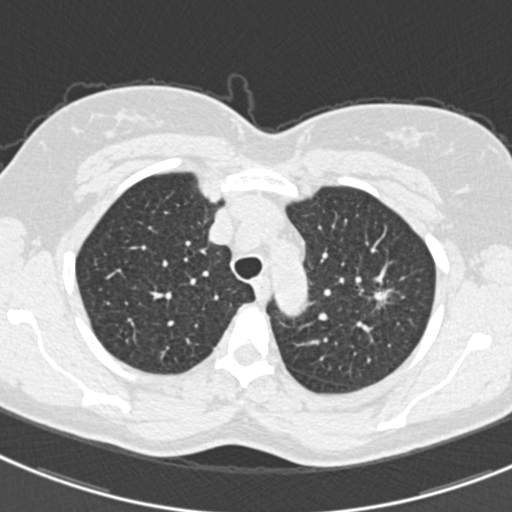
Low-dose screening chest CT, one axial slice. Slice 247 of 309 in the series (ordered by position). Reconstruction kernel B30f. 120 kVp. Lung window (W 1500 / L -600 HU). 1 mm slice thickness. 512 × 512 image matrix, field of view 302 × 302 mm.
Structures marked on this image (expert manual segmentation):
- lesion 1 (tumor, upper lobe of left lung): bounding box <374,290,391,304> (left, top, right, bottom; pixels)